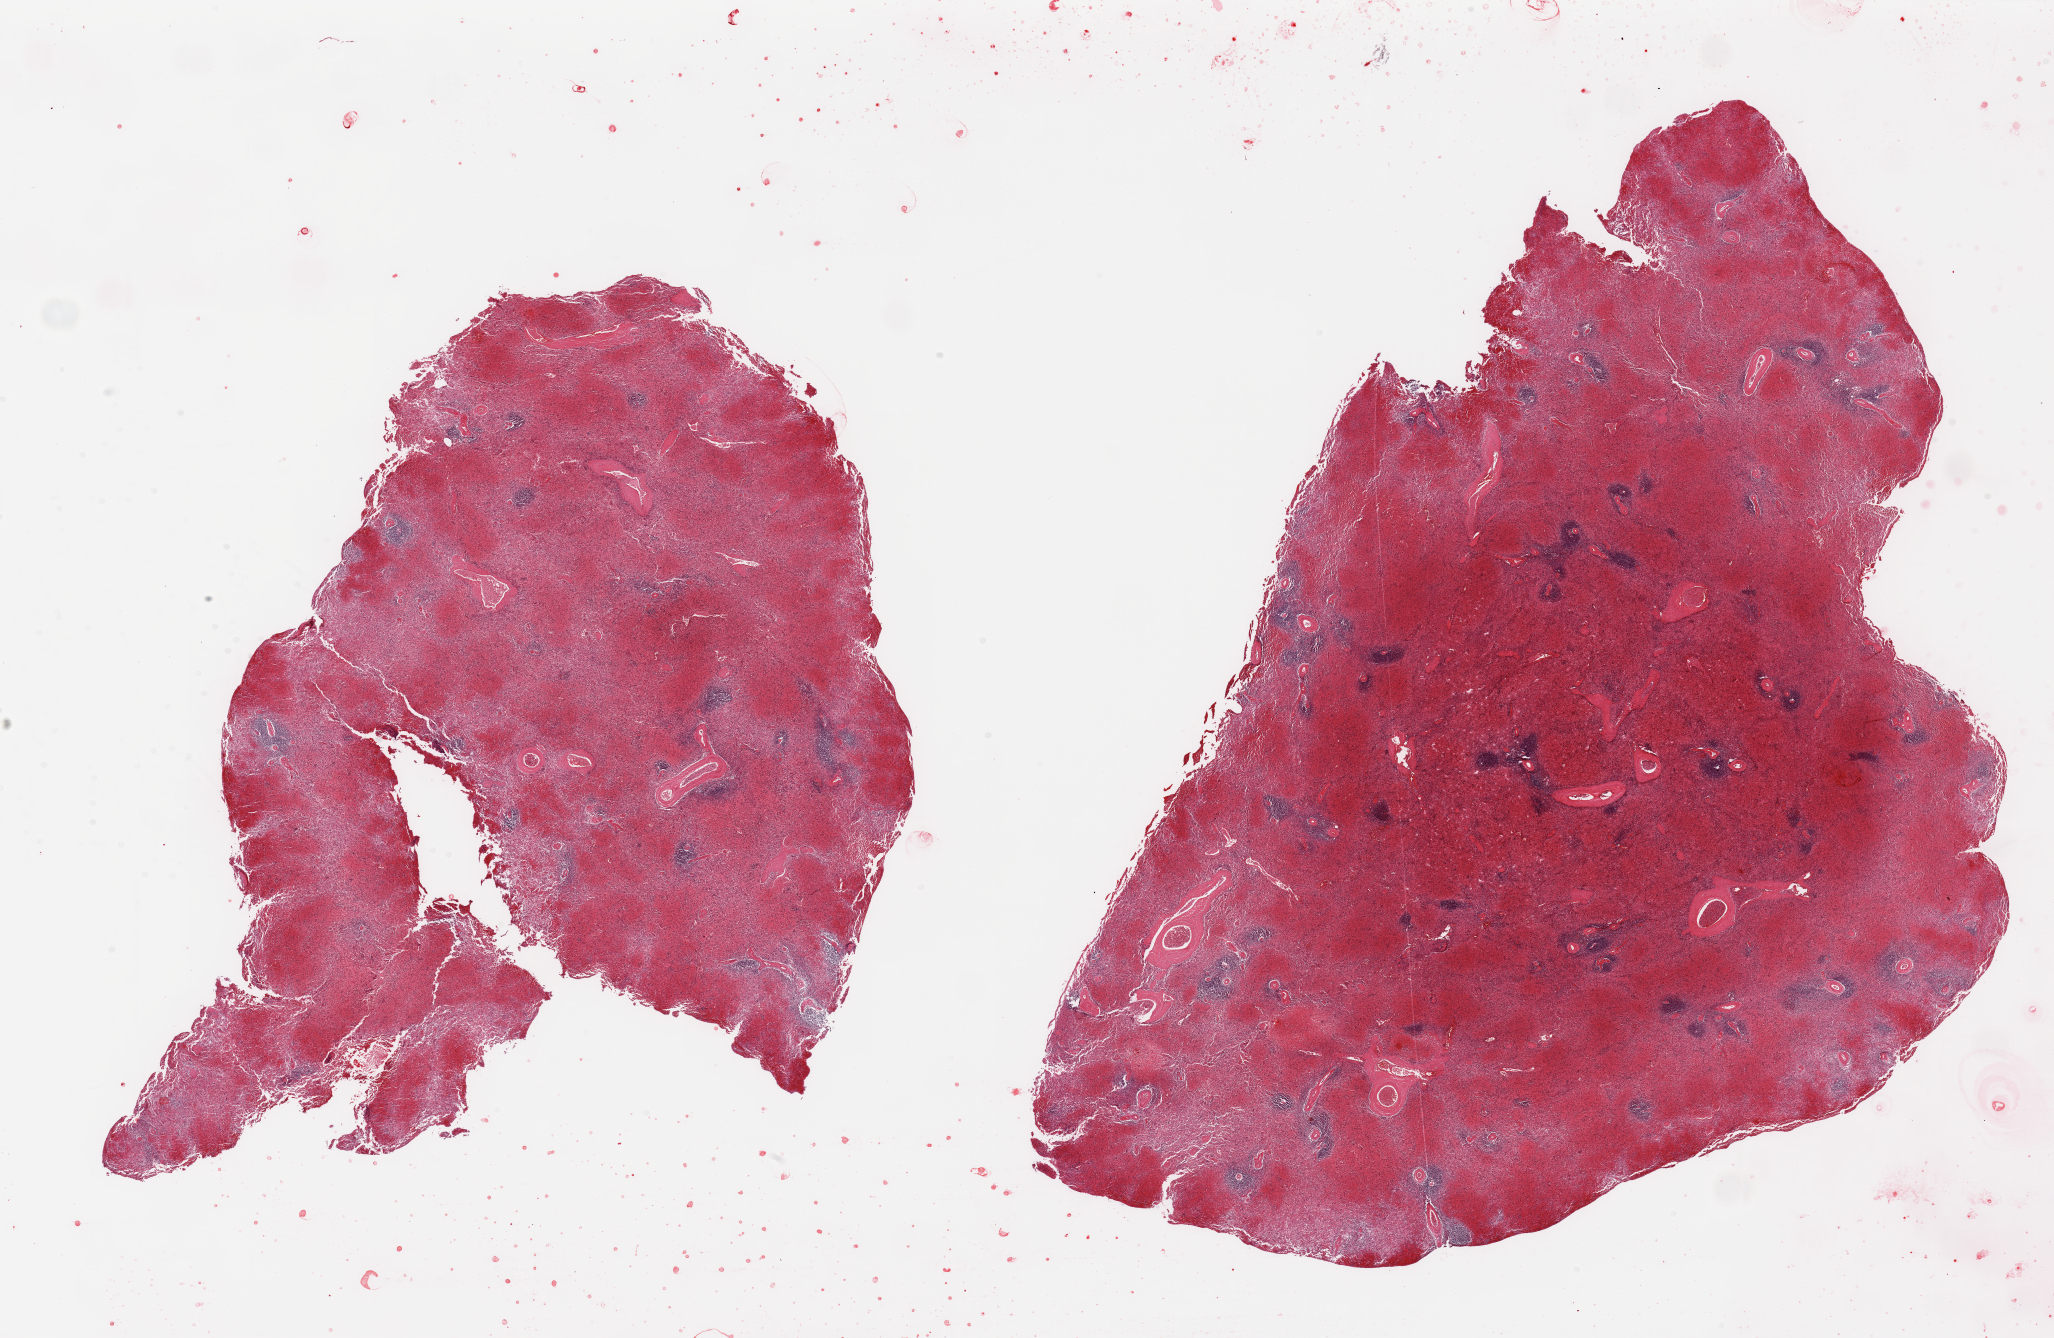
H&E whole-slide image — a low-resolution overview of the entire scanned area, about 32.5 x 21.2 mm; PAXgene-fixed paraffin-embedded (PFPE) section; target tissue: spleen; donor tissue sample. Female donor.
- reviewer comment on this tissue sample: 2 pieces; severe congestion